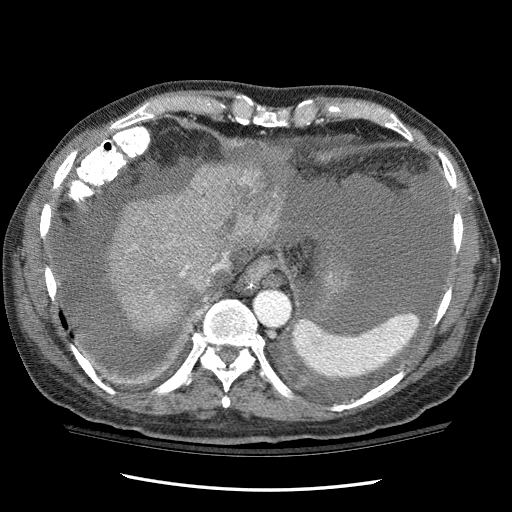
Contrast-enhanced abdominal CT (liver protocol), one axial slice. Position 92 of 114 along the scan axis. Reconstruction kernel STANDARD. One of 3 acquisitions stored at this slice position. Soft-tissue window (W 400 / L 40 HU). 2.5 mm slice thickness. 512 × 512 image matrix. Case-level facts recorded for this patient, not image findings: diagnosis: hepatocellular carcinoma (patient treated with transarterial chemoembolisation; whether this scan precedes or follows treatment is not stated here); TNM stage (as recorded): Stage-I; Child-Pugh class: C.
Structures marked on this image (semi-automatically segmented with operator editing):
- liver parenchyma outside the tumour (the mass and vessels are separate outlines, so this box may not span the whole liver): bounding box [x1, y1, x2, y2] px = [108, 160, 286, 327]
- mass: [191, 168, 284, 236]
- liver vessels: [181, 264, 222, 275]